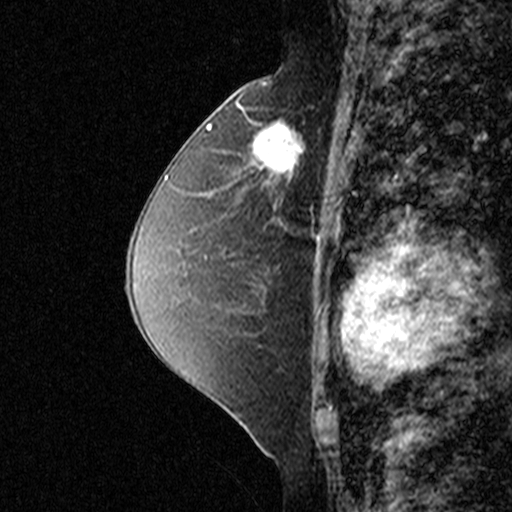
Breast MRI (dynamic contrast-enhanced), one sagittal slice. Slice 24 of 44 in the series (ordered by position). Dynamic contrast-enhanced study with each time point stored as its own series, time point 2 of 3 at this slice position (early post-contrast, ordered by acquisition time). 1.5 T. TE 4.5 ms, TR 11 ms. 3 mm slice thickness. 512 × 512 image matrix, field of view 200 × 200 mm. Patient: female, 49 years. Case-level facts recorded for this patient, not image findings: setting: breast cancer imaged before/during neoadjuvant chemotherapy; receptor status: triple-negative.
Structures marked on this image (semi-automatic segmentation, software-assisted and operator-edited):
- analysis volume of interest (the breast-tissue region the enhancement analysis was run in; not a lesion): box from (x=240, y=100) to (x=335, y=197) px
- tumour enhancement mask (voxels above the 90 % enhancement threshold inside the analysis volume of interest): (x=258, y=118)–(x=306, y=187)